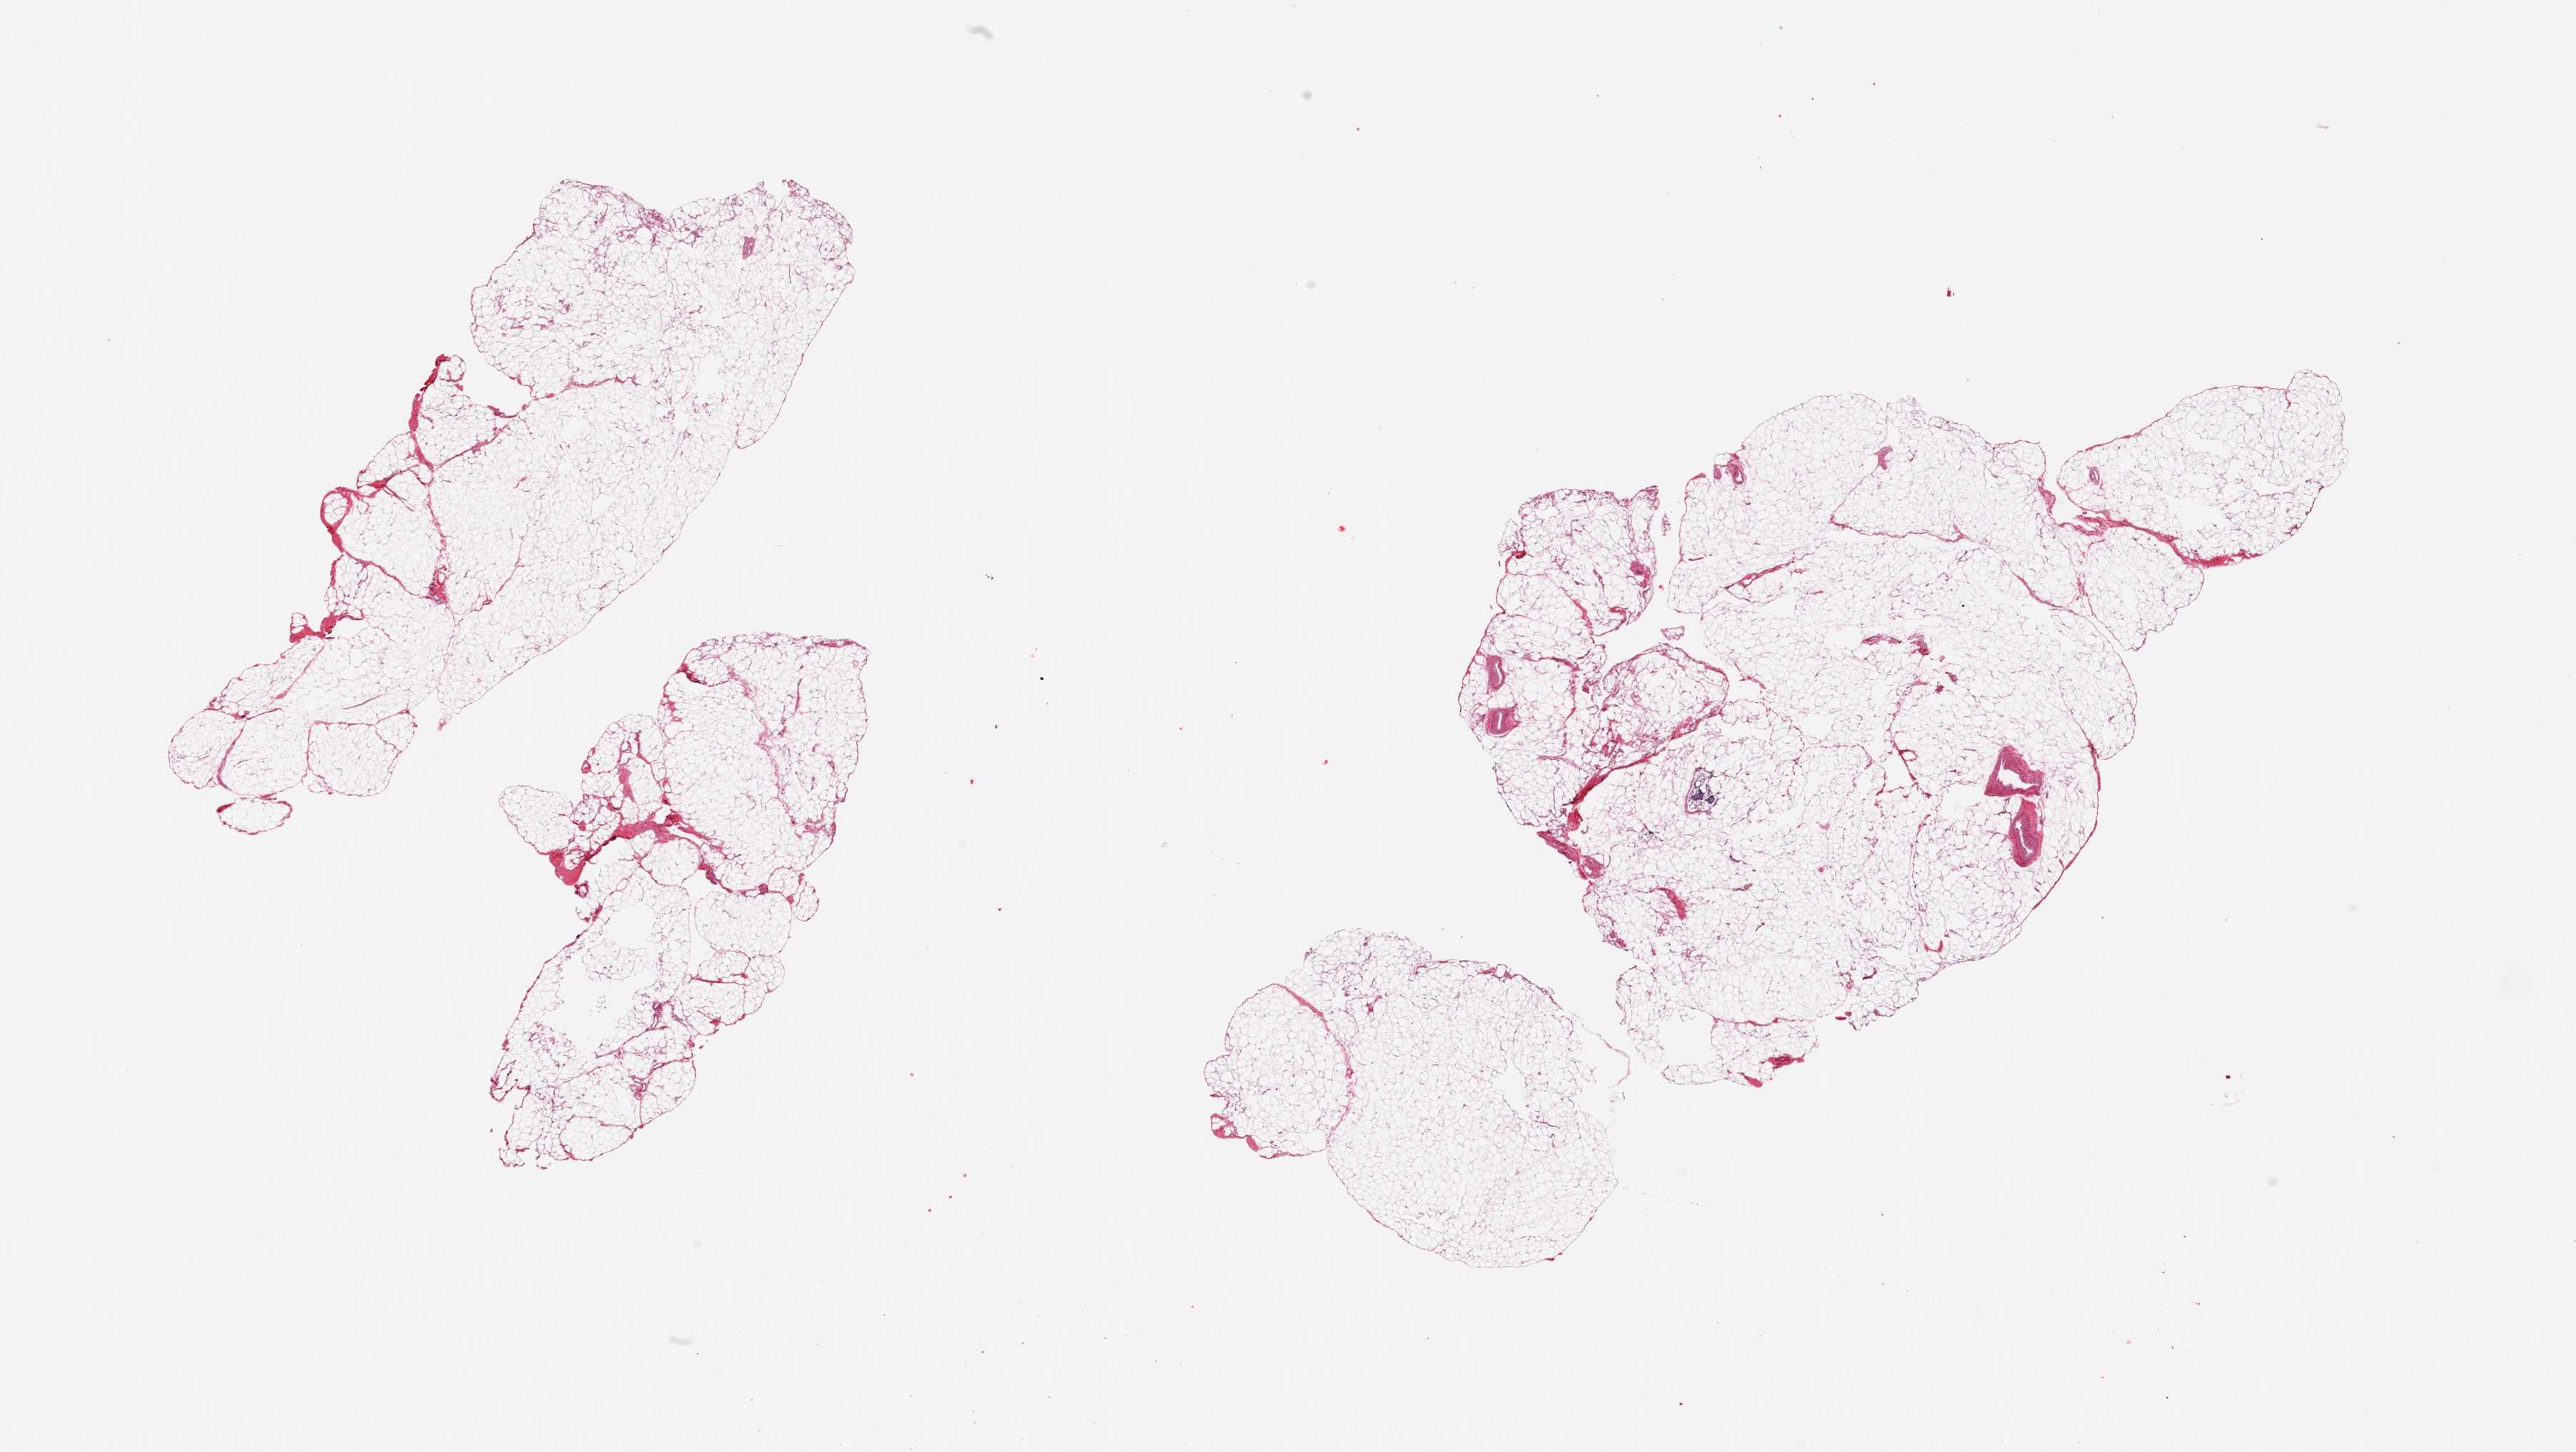
Haematoxylin and eosin whole-slide image — whole scanned area (about 28.5 x 16.1 mm, slide scanned at 20x) shown as a low-resolution overview. PAXgene-fixed, paraffin-embedded tissue. Target tissue: omentum. Donor tissue sample. Donor: female.
Reviewer comment on this tissue sample: 2 pieces, ~5% vascular elements.